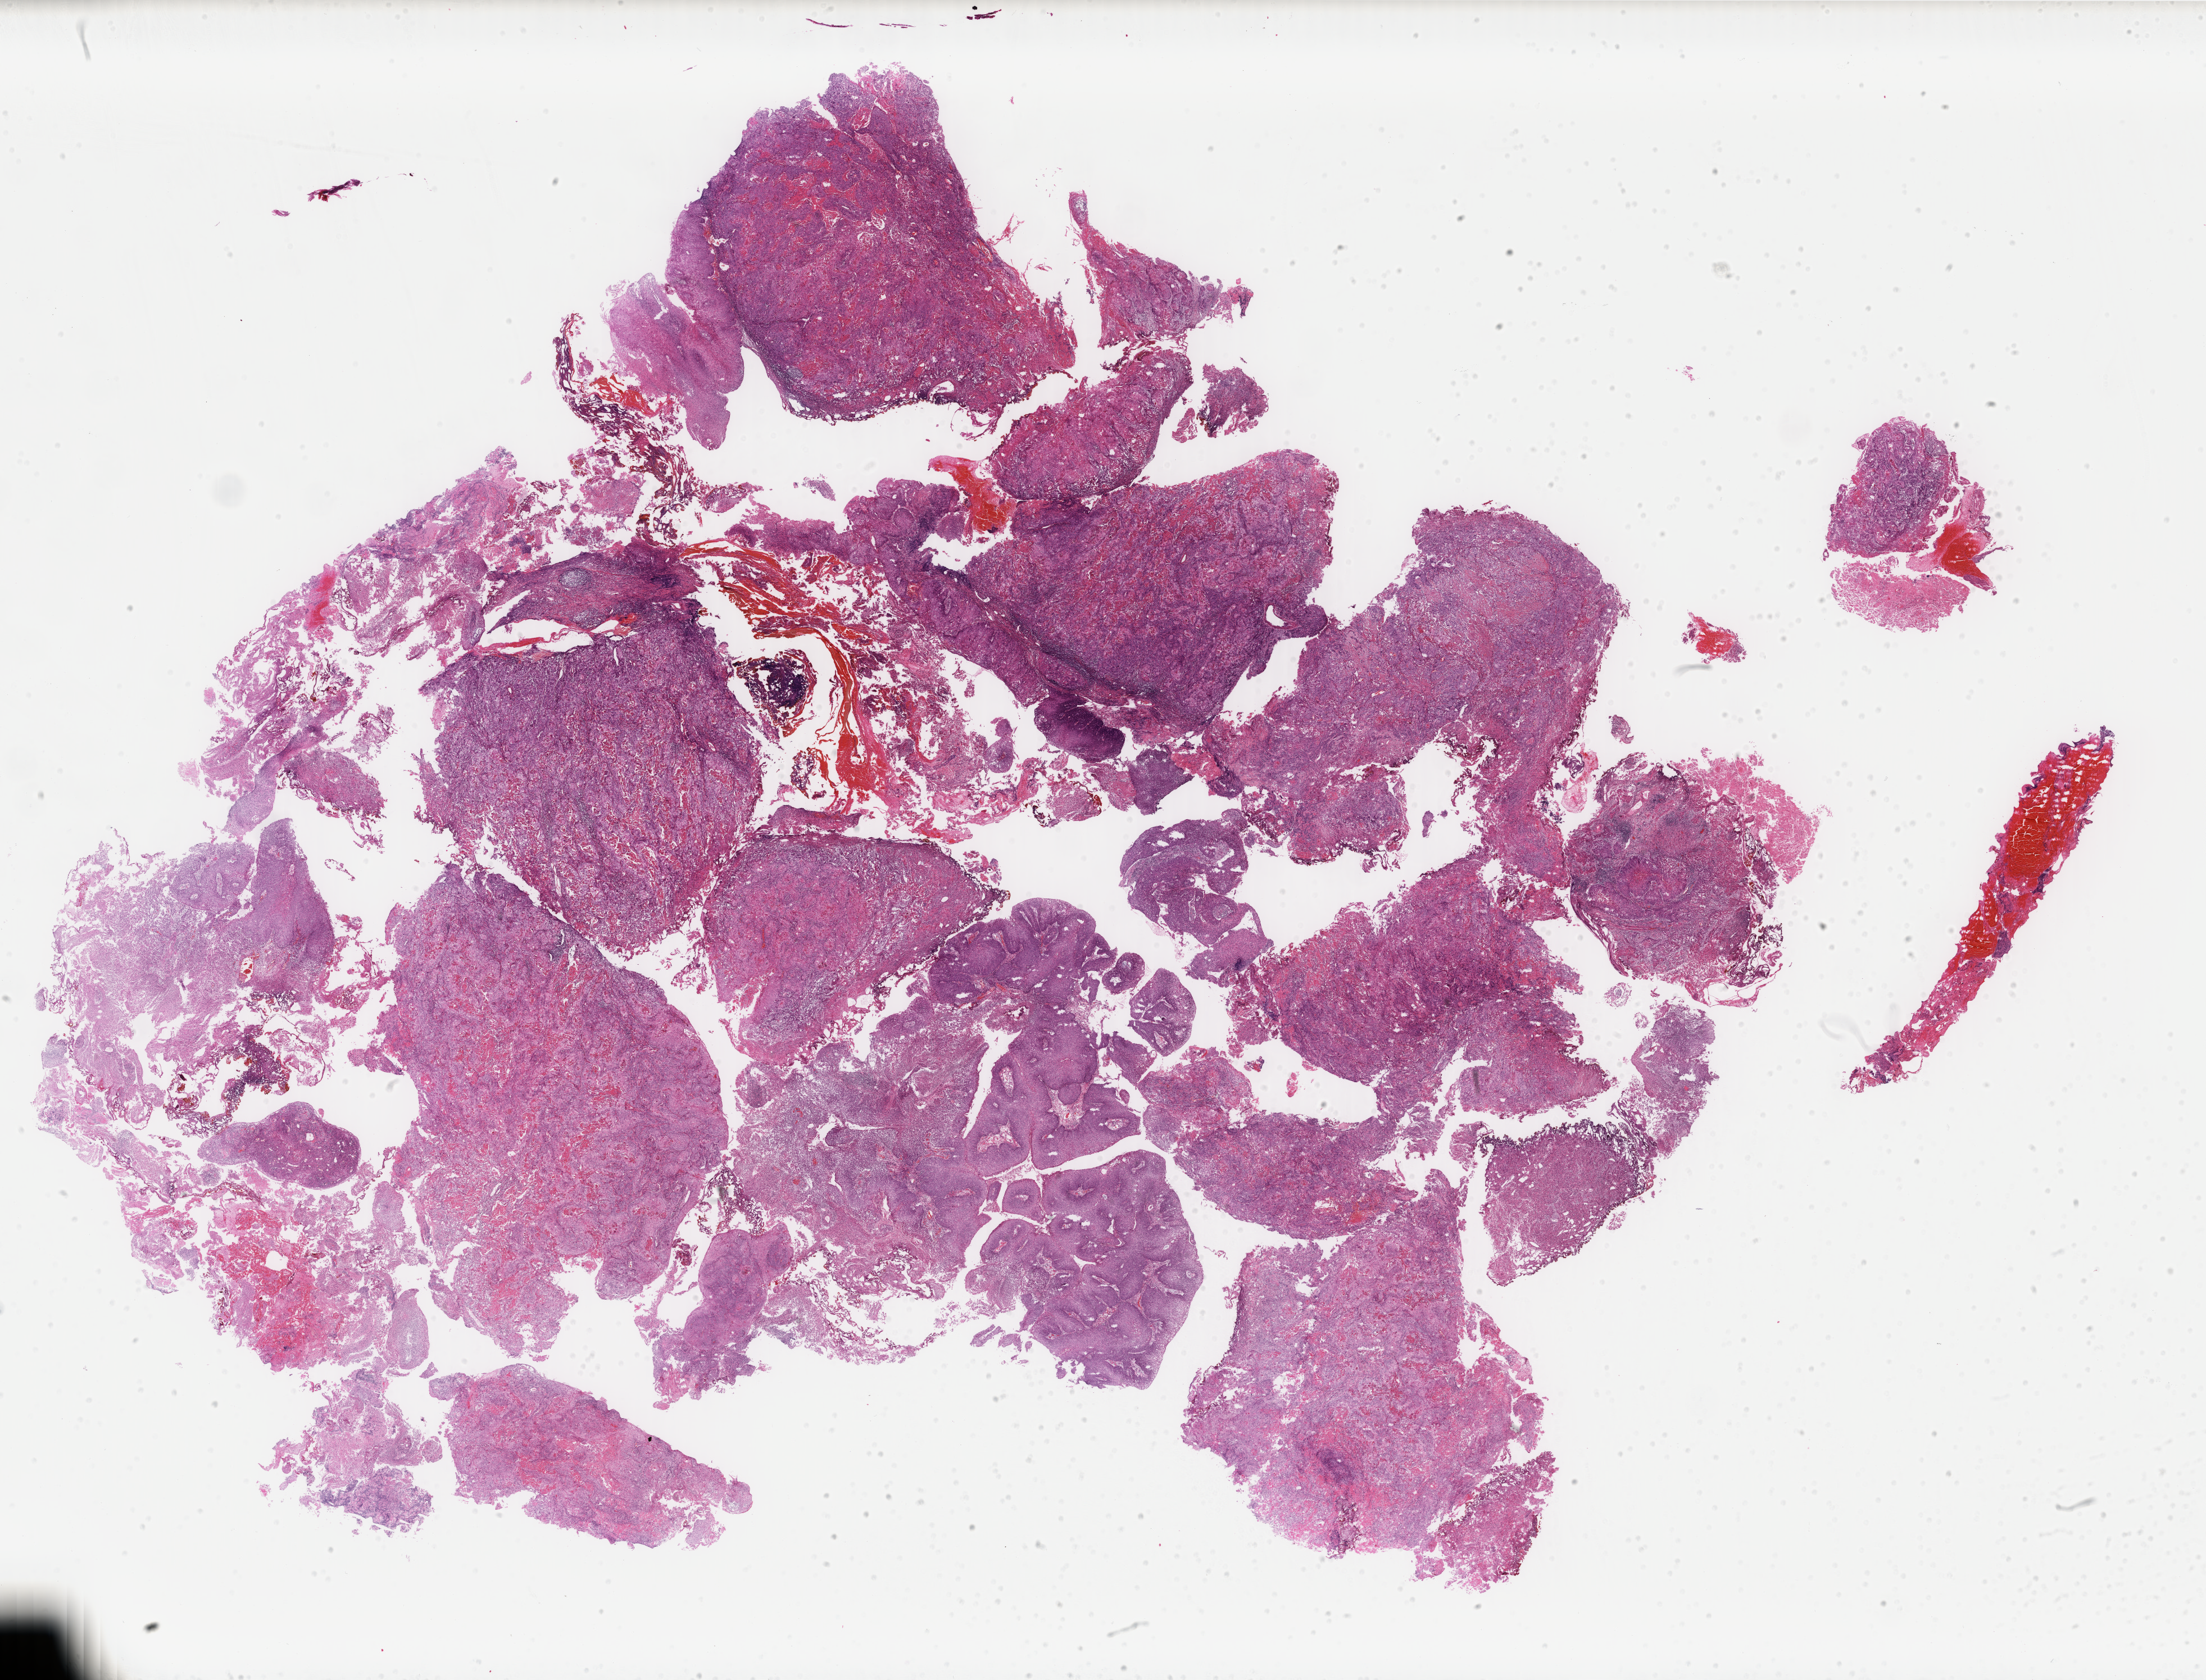
Digitized Hematoxylin and eosin (H&E) stained tissue section (whole slide), a low-resolution overview of the entire scanned area, about 31.2 x 23.7 mm (slide scanned at 40x), formalin-fixed paraffin-embedded (FFPE) diagnostic section, sample: primary tumour, bladder. Patient: female, age at initial diagnosis 56 years. Histologic grade: high grade.
TNM: N0 M0. Diagnosis: Transitional cell carcinoma. AJCC pathologic stage: II.